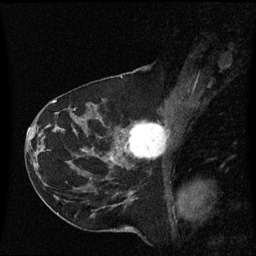
Breast MRI (dynamic contrast-enhanced), one sagittal slice. Position 32 of 60 along the scan axis. Dynamic contrast-enhanced series, image 2 of 3 at this slice position (ordered by acquisition). 1.5 T. TE 4.2 ms, TR 8.4 ms. 256 × 256 image matrix. Patient: female, 41 years. Case-level facts recorded for this patient, not image findings: setting: breast cancer imaged before/during neoadjuvant chemotherapy; receptor status: triple-negative.
Annotated regions visible in this slice (semi-automatic segmentation, software-assisted and operator-edited):
- analysis volume of interest (the breast-tissue region the enhancement analysis was run in; not a lesion): bounding box [x1, y1, x2, y2] px = [116, 122, 168, 169]
- tumour enhancement mask (voxels above the 70 % enhancement threshold inside the analysis volume of interest): [128, 124, 166, 159]